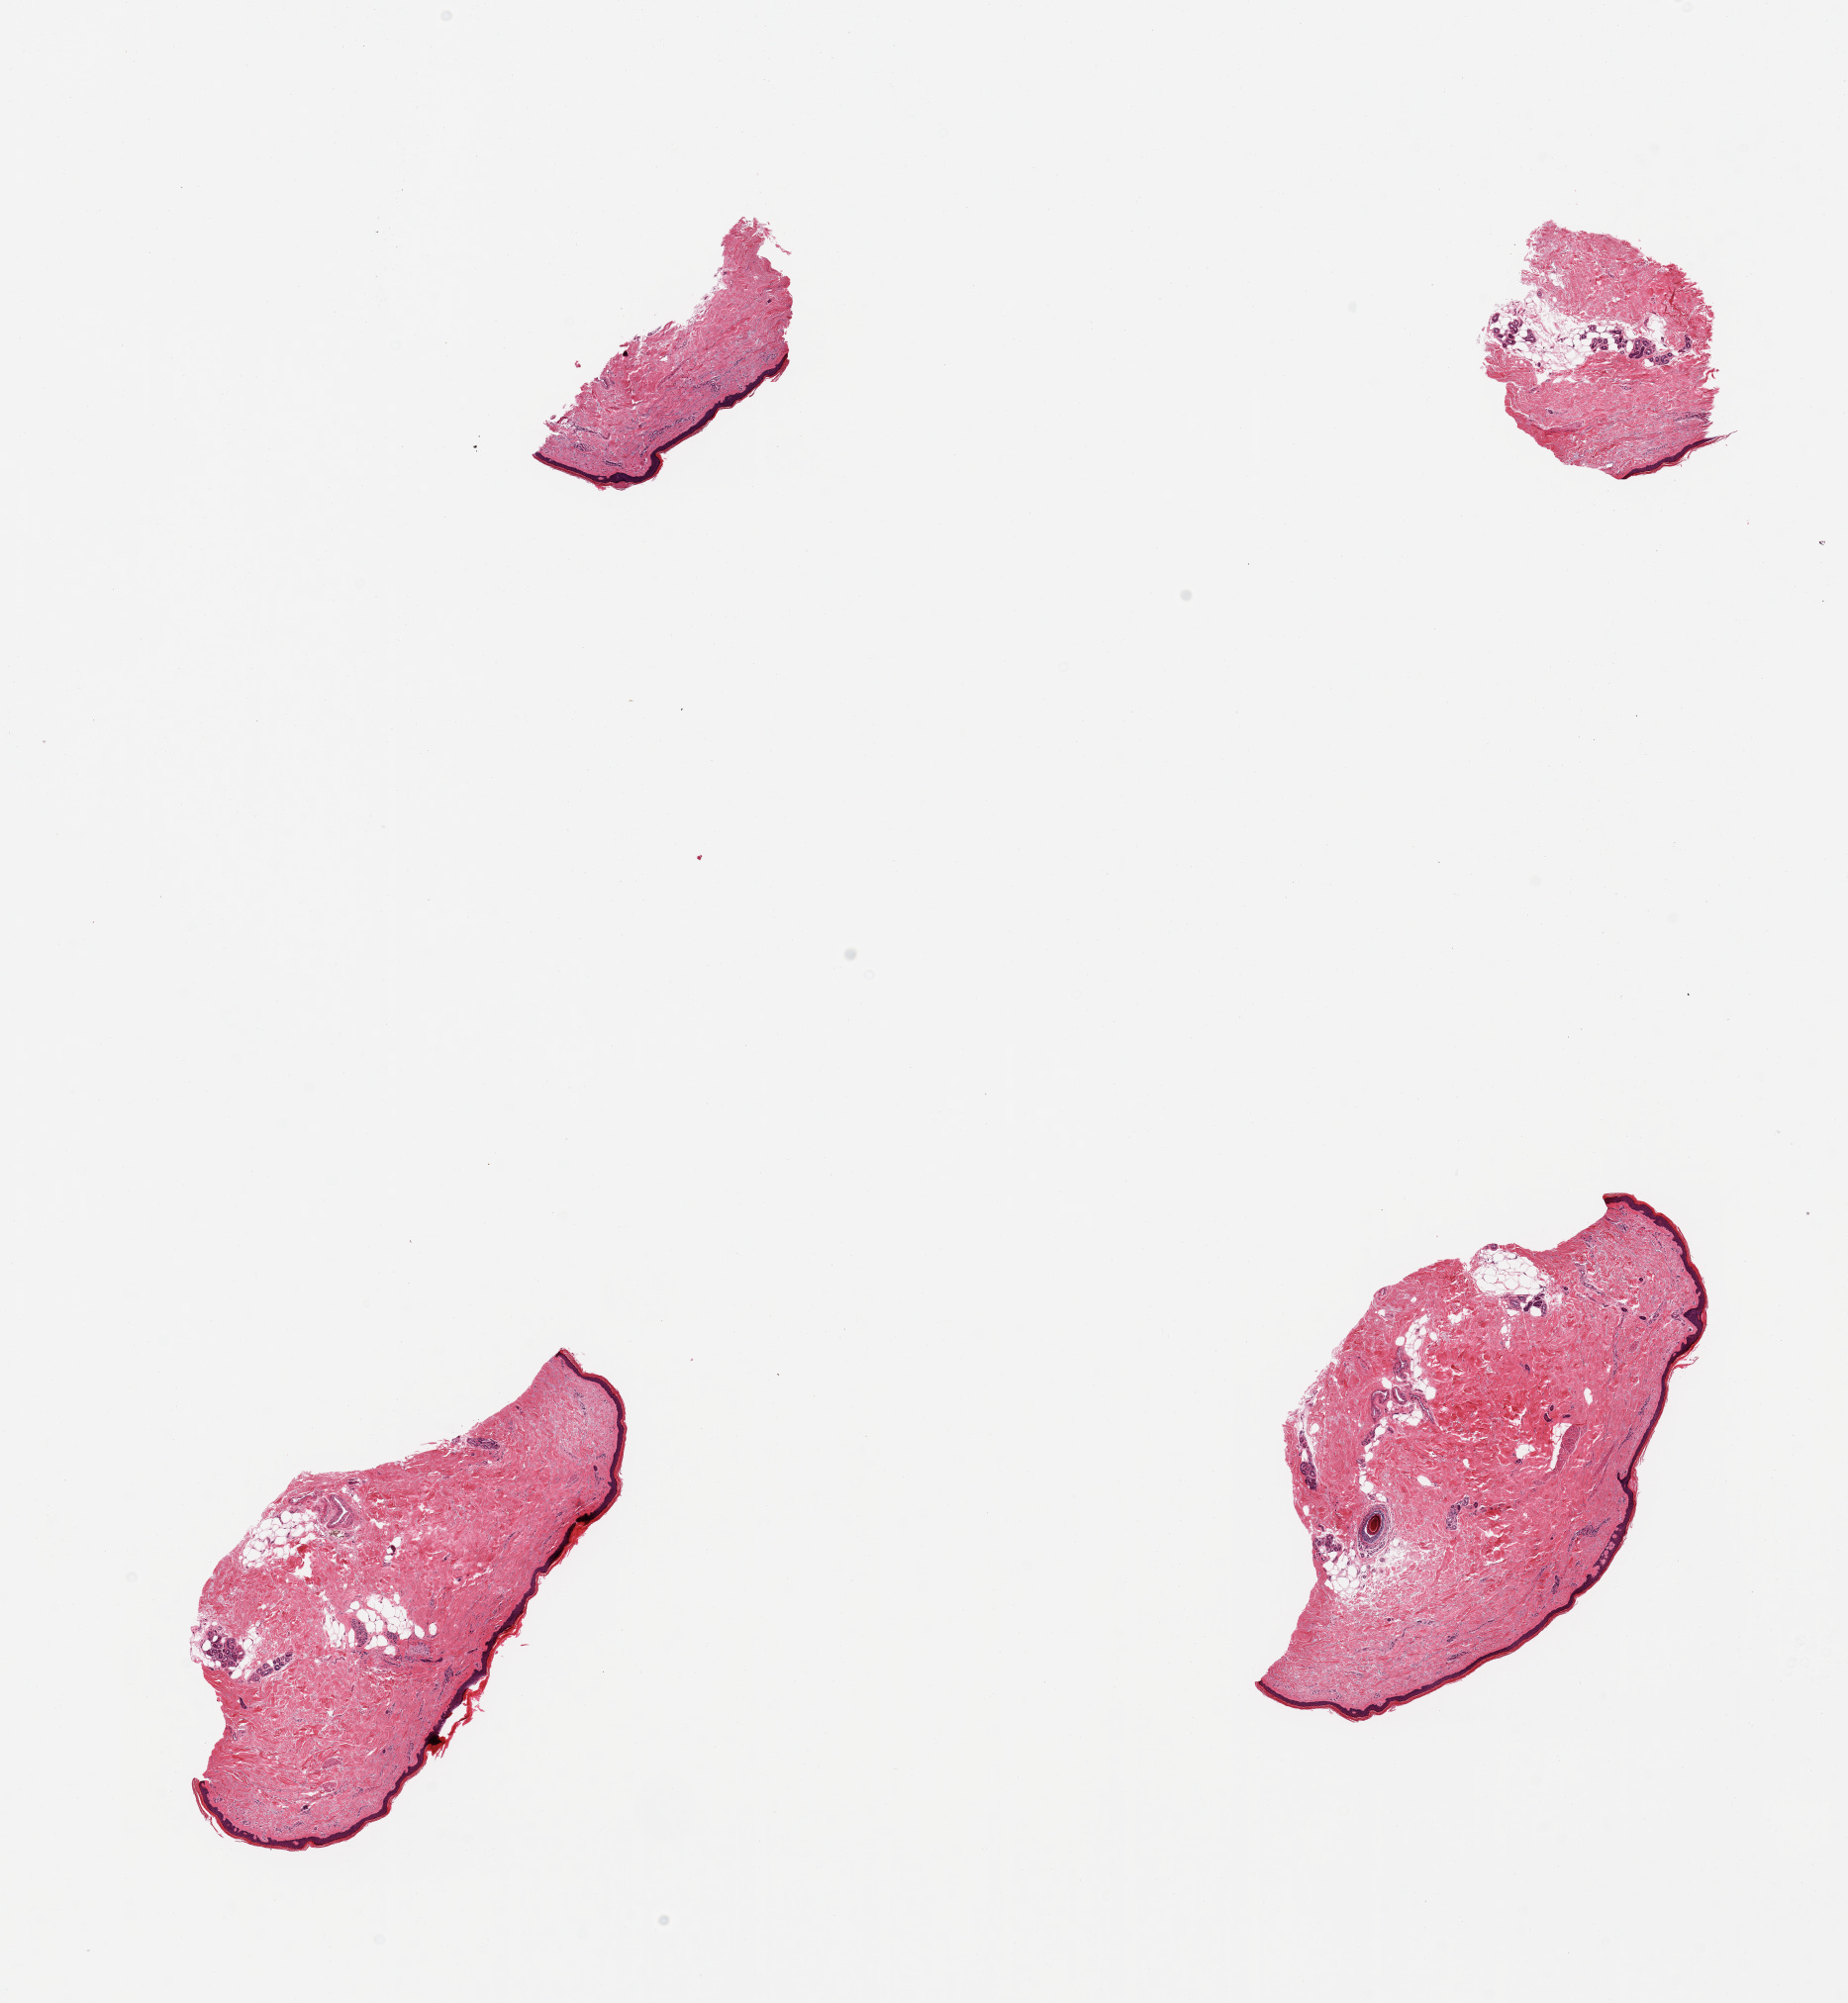
Digitized hematoxylin and eosin (H&E)-stained section, brightfield, a low-resolution overview of the entire scanned area, about 14.8 x 16.0 mm (slide scanned at 20x); PAXgene-fixed paraffin-embedded (PFPE) section; sampled site (target tissue): skin of lower leg; tissue donor sample.
Pathologist's review note for this sample: 4 small pieces; up to 20% dermal fat.